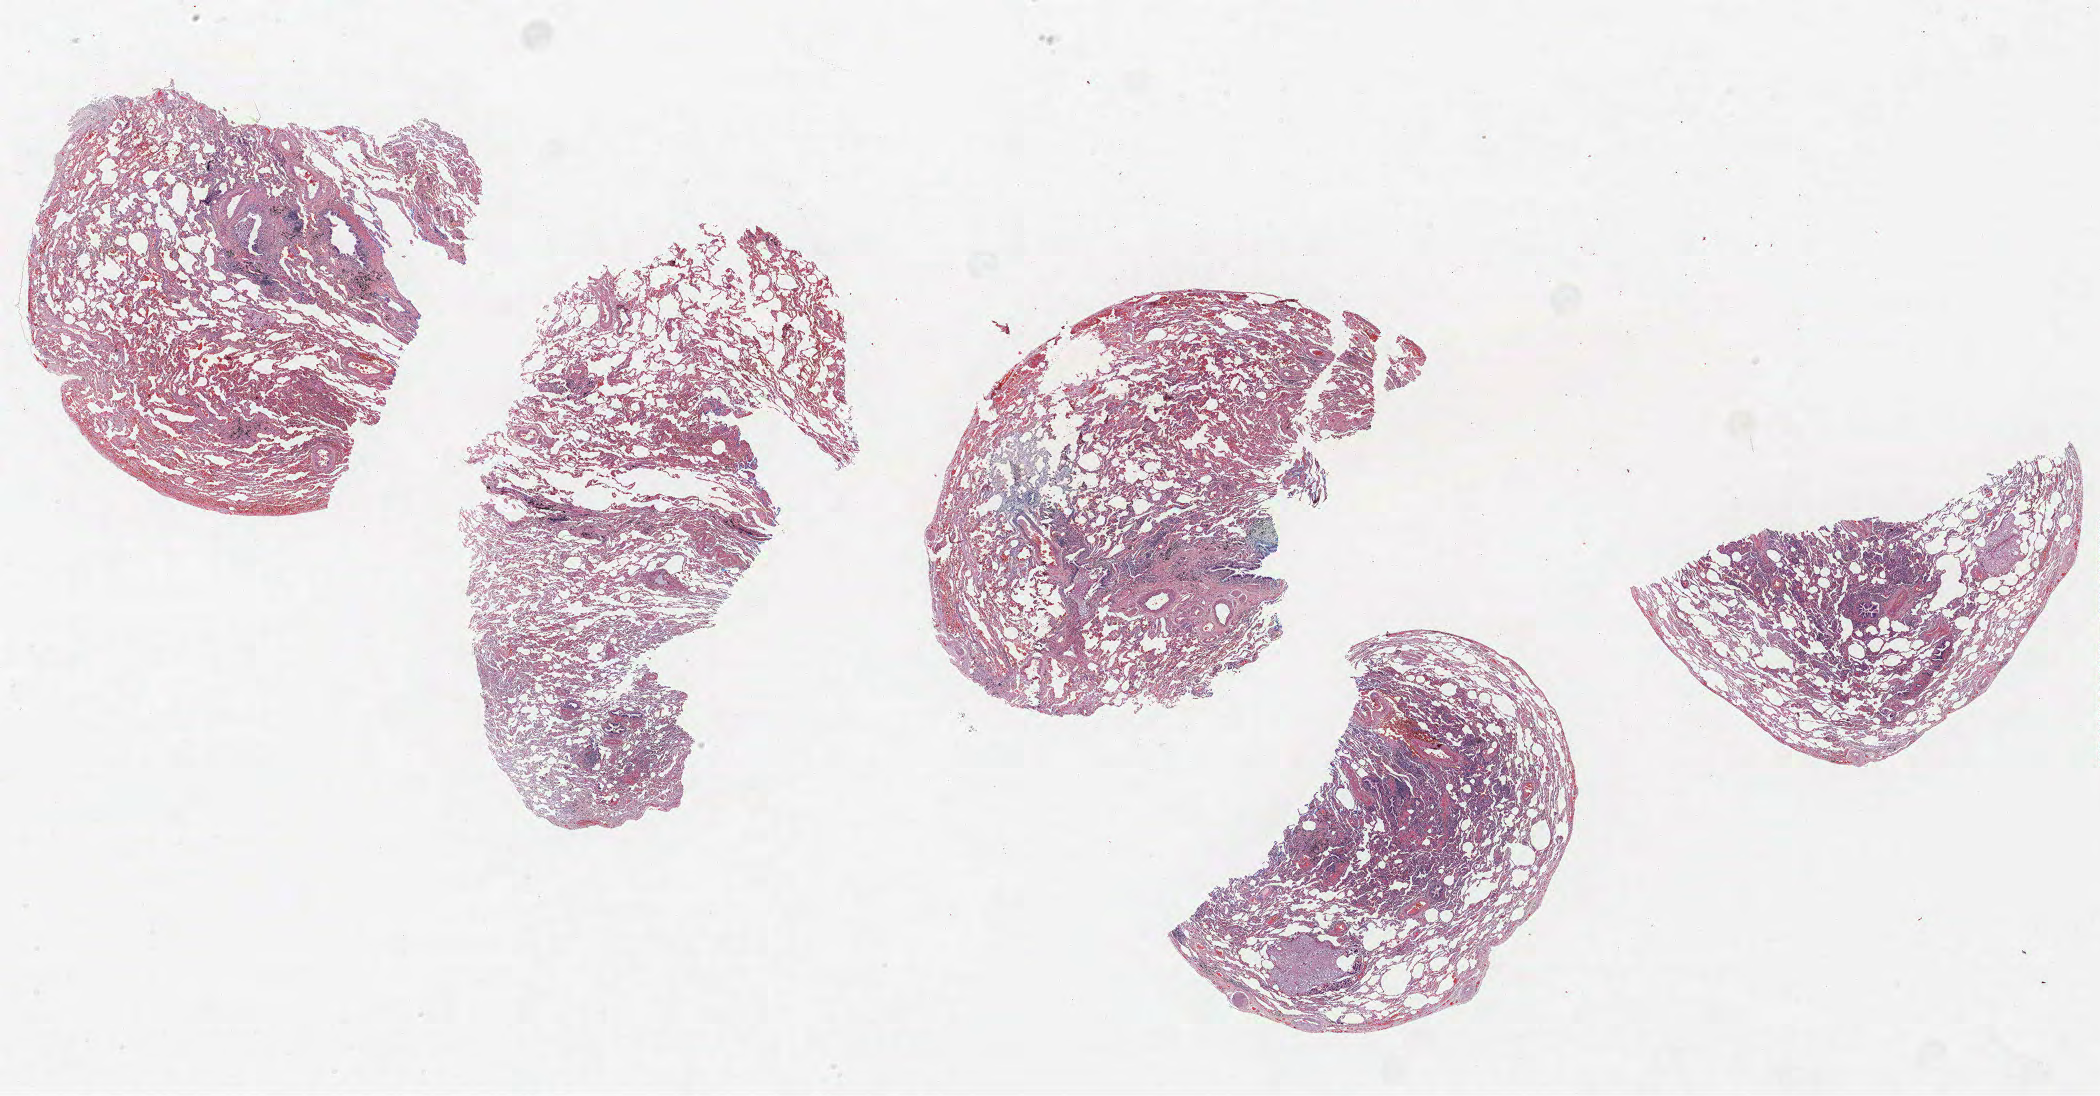
Whole-slide histology image, H&E-stained — a low-resolution overview of the entire scanned area, about 33.6 x 17.5 mm (slide scanned at 40x), FFPE section, lung tissue. Male, age 67 at enrolment. Former smoker at enrolment. Grade: moderately differentiated (G2).
Primary tumour location (clinical record): right lower lobe. Tumour size (pathology): 12 mm. Stage (AJCC 6th edition): IA. Participant's lung-cancer diagnosis: Adenocarcinoma, NOS.